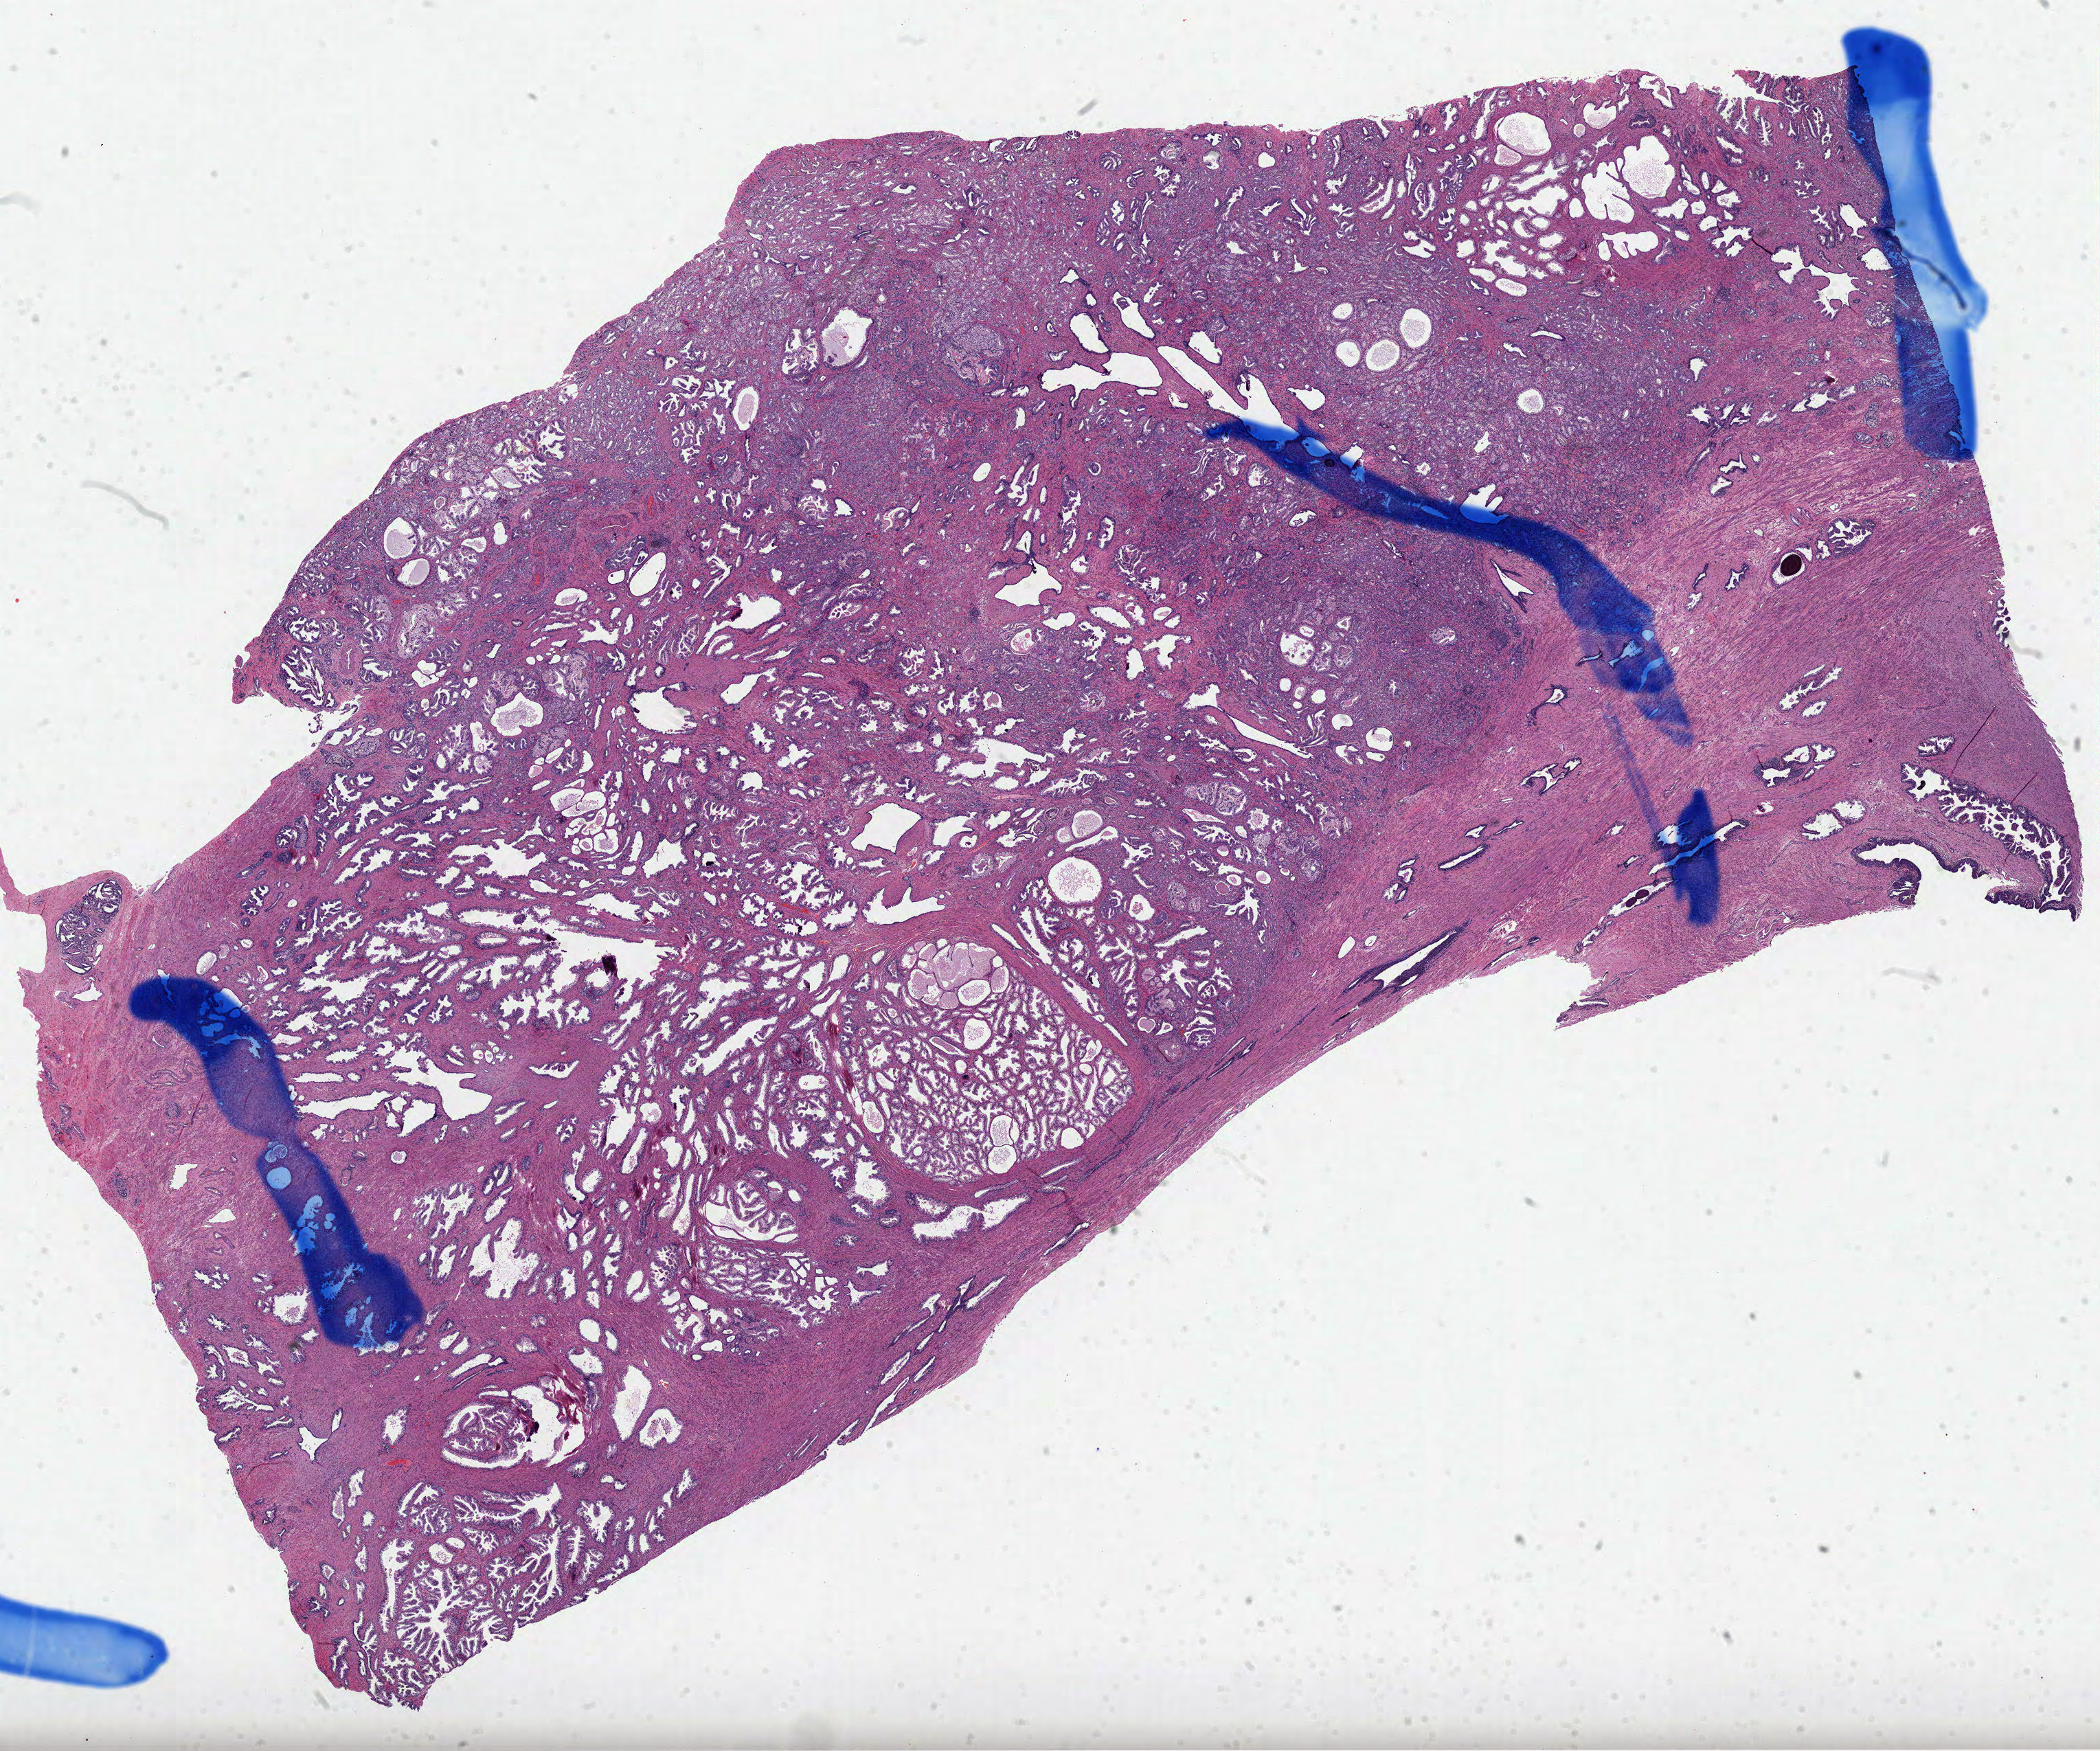
Whole-slide histology image, H&E, low-resolution overview of the scanned area, about 24.7 x 20.6 mm (slide scanned at 40x); formalin-fixed paraffin-embedded (FFPE) diagnostic section; primary tumour sample from the prostate. Male patient; age at initial diagnosis 60 years. Gleason score: 7 (3+4).
Pathologic diagnosis: Acinar cell carcinoma (prostate gland). Lymph nodes positive (case pathology): 0 of 17 examined. Laterality: bilateral.